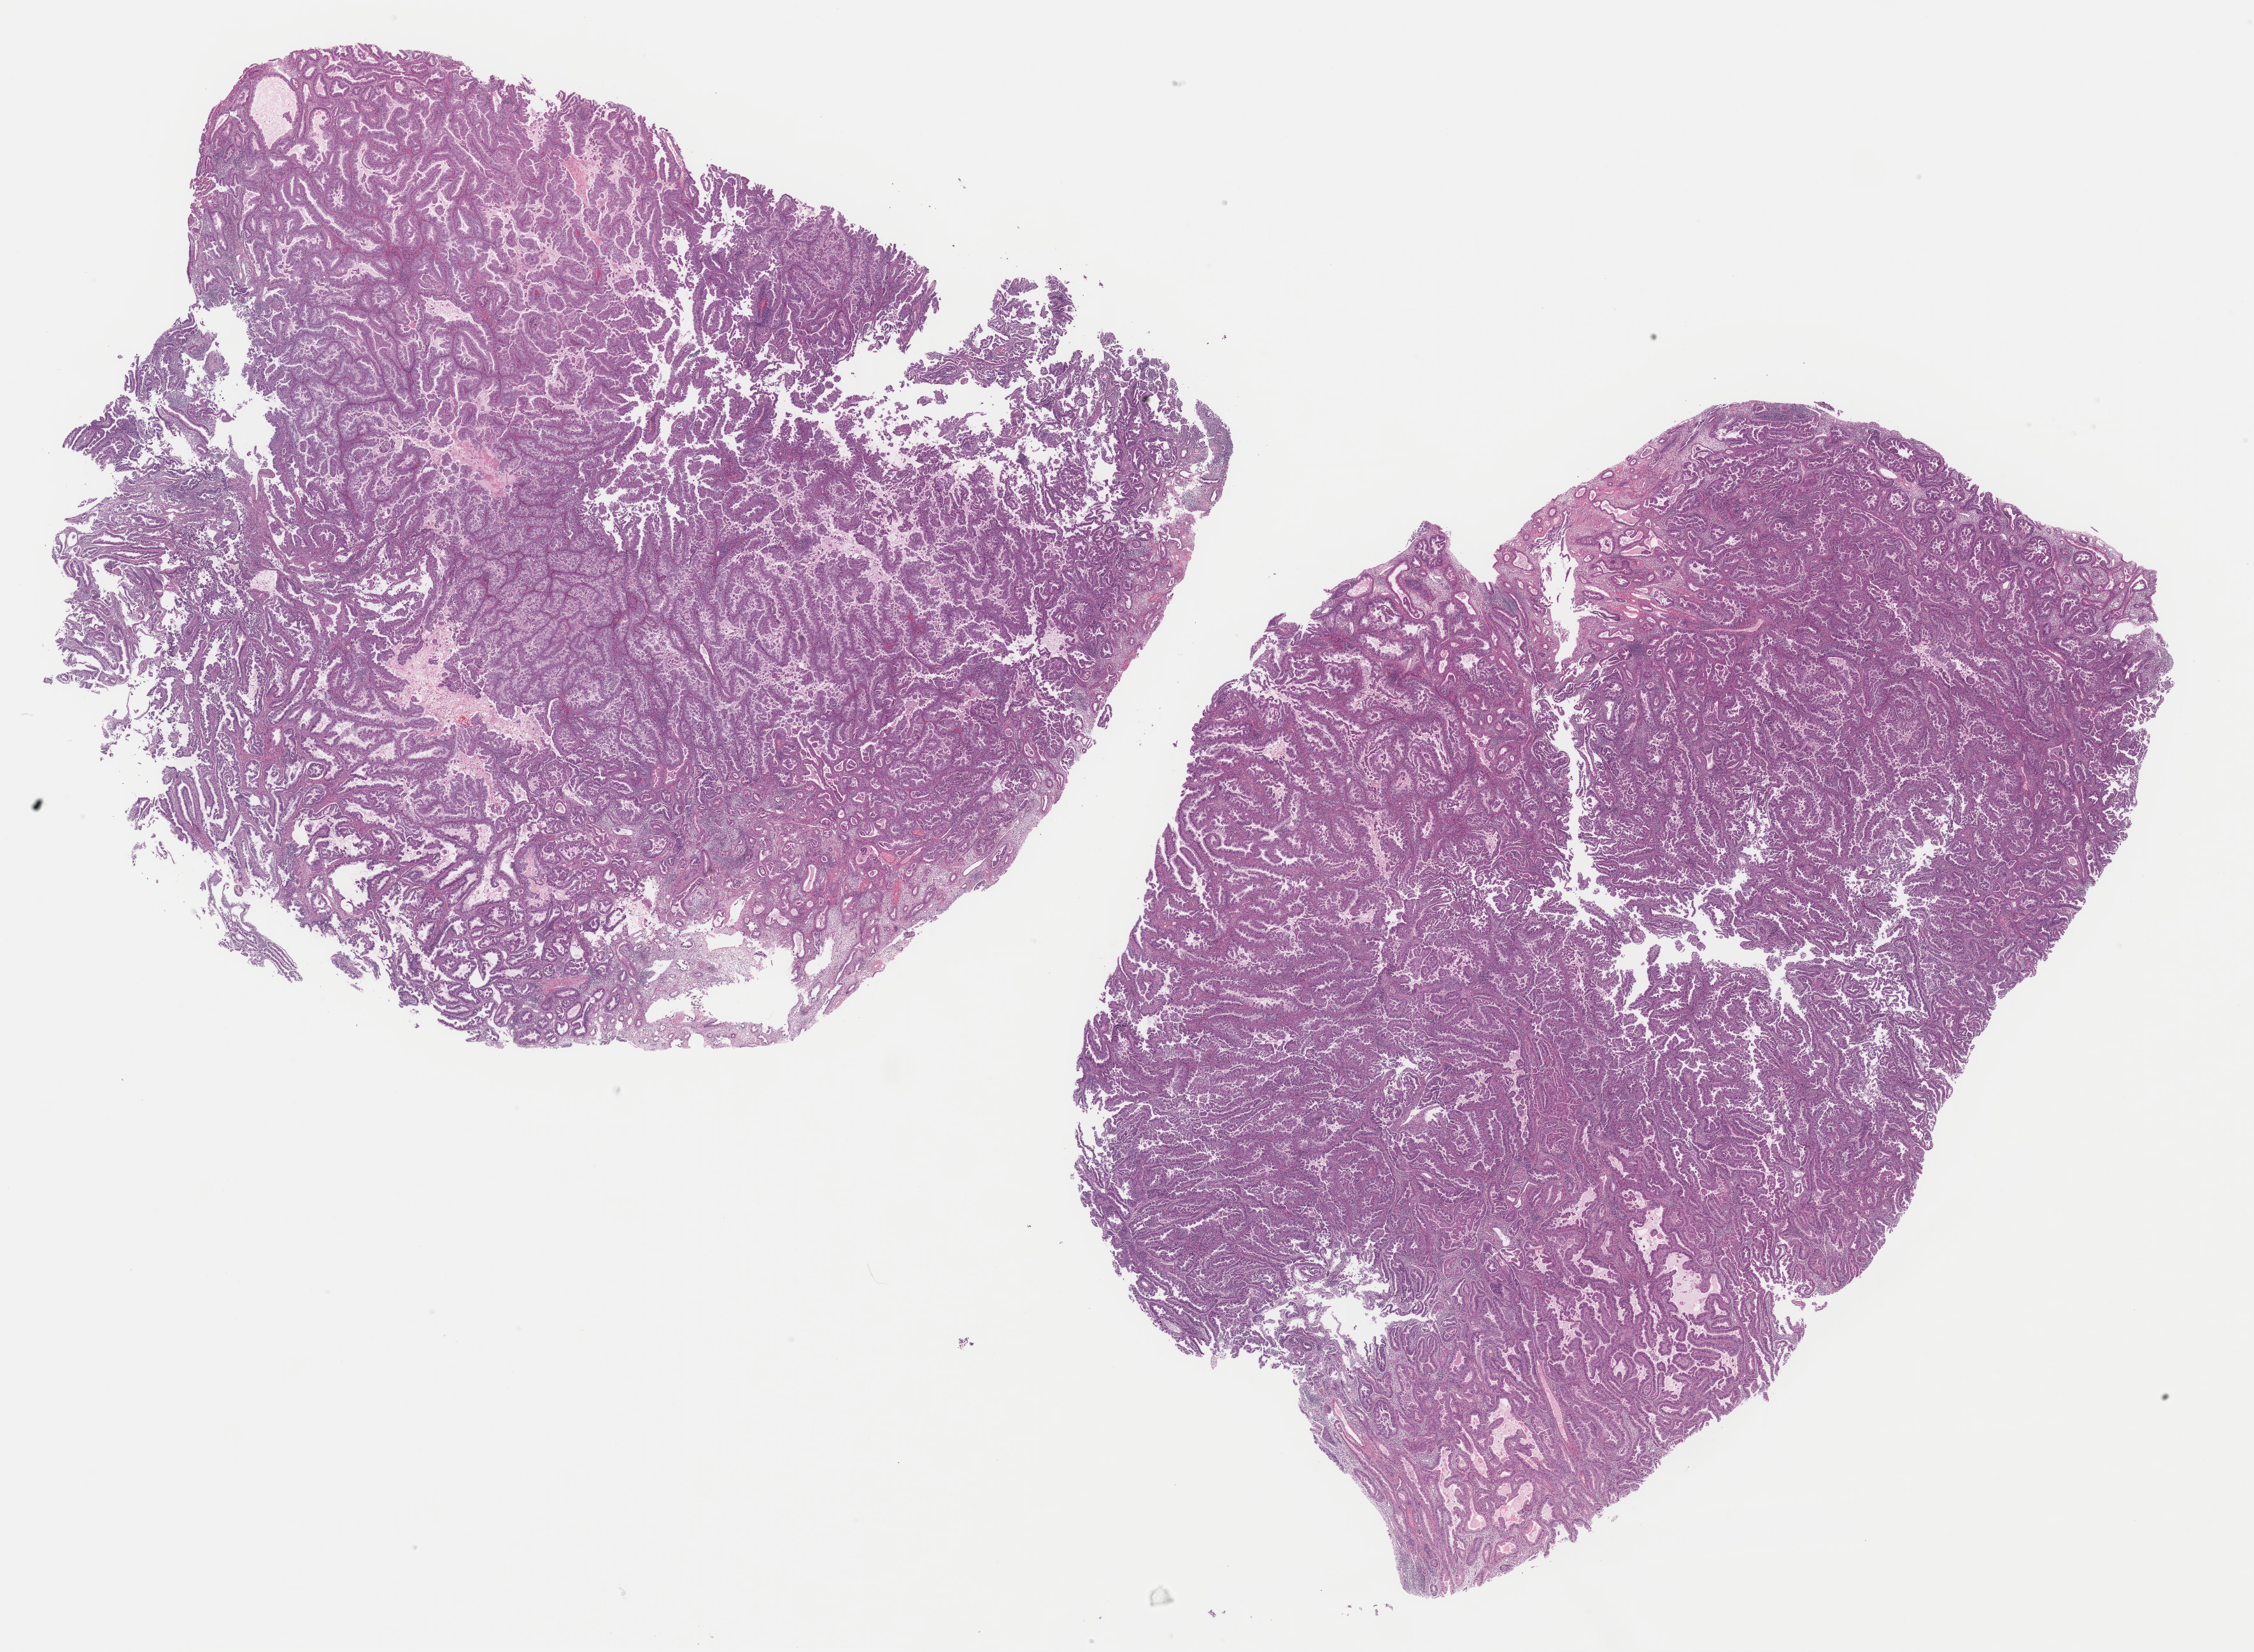
Digitized H&E-stained tissue section (whole slide) — low-resolution overview of the scanned area, about 28.0 x 20.5 mm. Formalin-fixed paraffin-embedded (FFPE) diagnostic section. Sample: primary tumour, uterus. Female, age 61 years at initial diagnosis. Histologic grade: G3 (poorly differentiated).
• FIGO stage: IA
• pathologic diagnosis: Serous cystadenocarcinoma, NOS